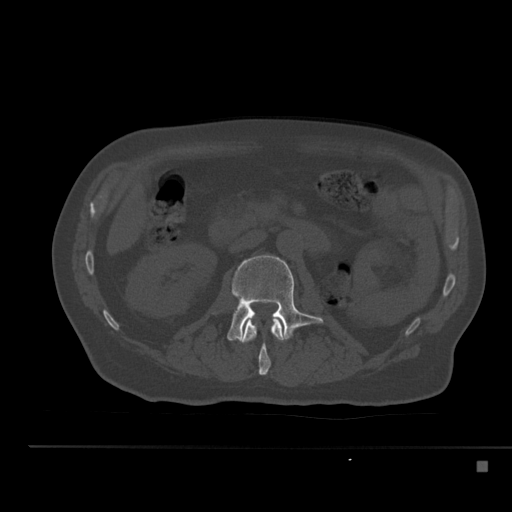
CT including the spine, one axial slice; position 192 of 517 along the scan axis; reconstruction kernel Br40s; 120 kVp; bone window (W 1800 / L 400 HU); 1.5 mm slice thickness; 512 × 512 image matrix. Male patient, age 70 years. Case-level facts recorded for this patient, not image findings: primary cancer: renal.
Outlined on this slice (semi-automatically segmented with operator editing):
- L1 vertebra: box from (x=240, y=317) to (x=287, y=375) px
- L2 vertebra: (x=227, y=254)–(x=324, y=341)